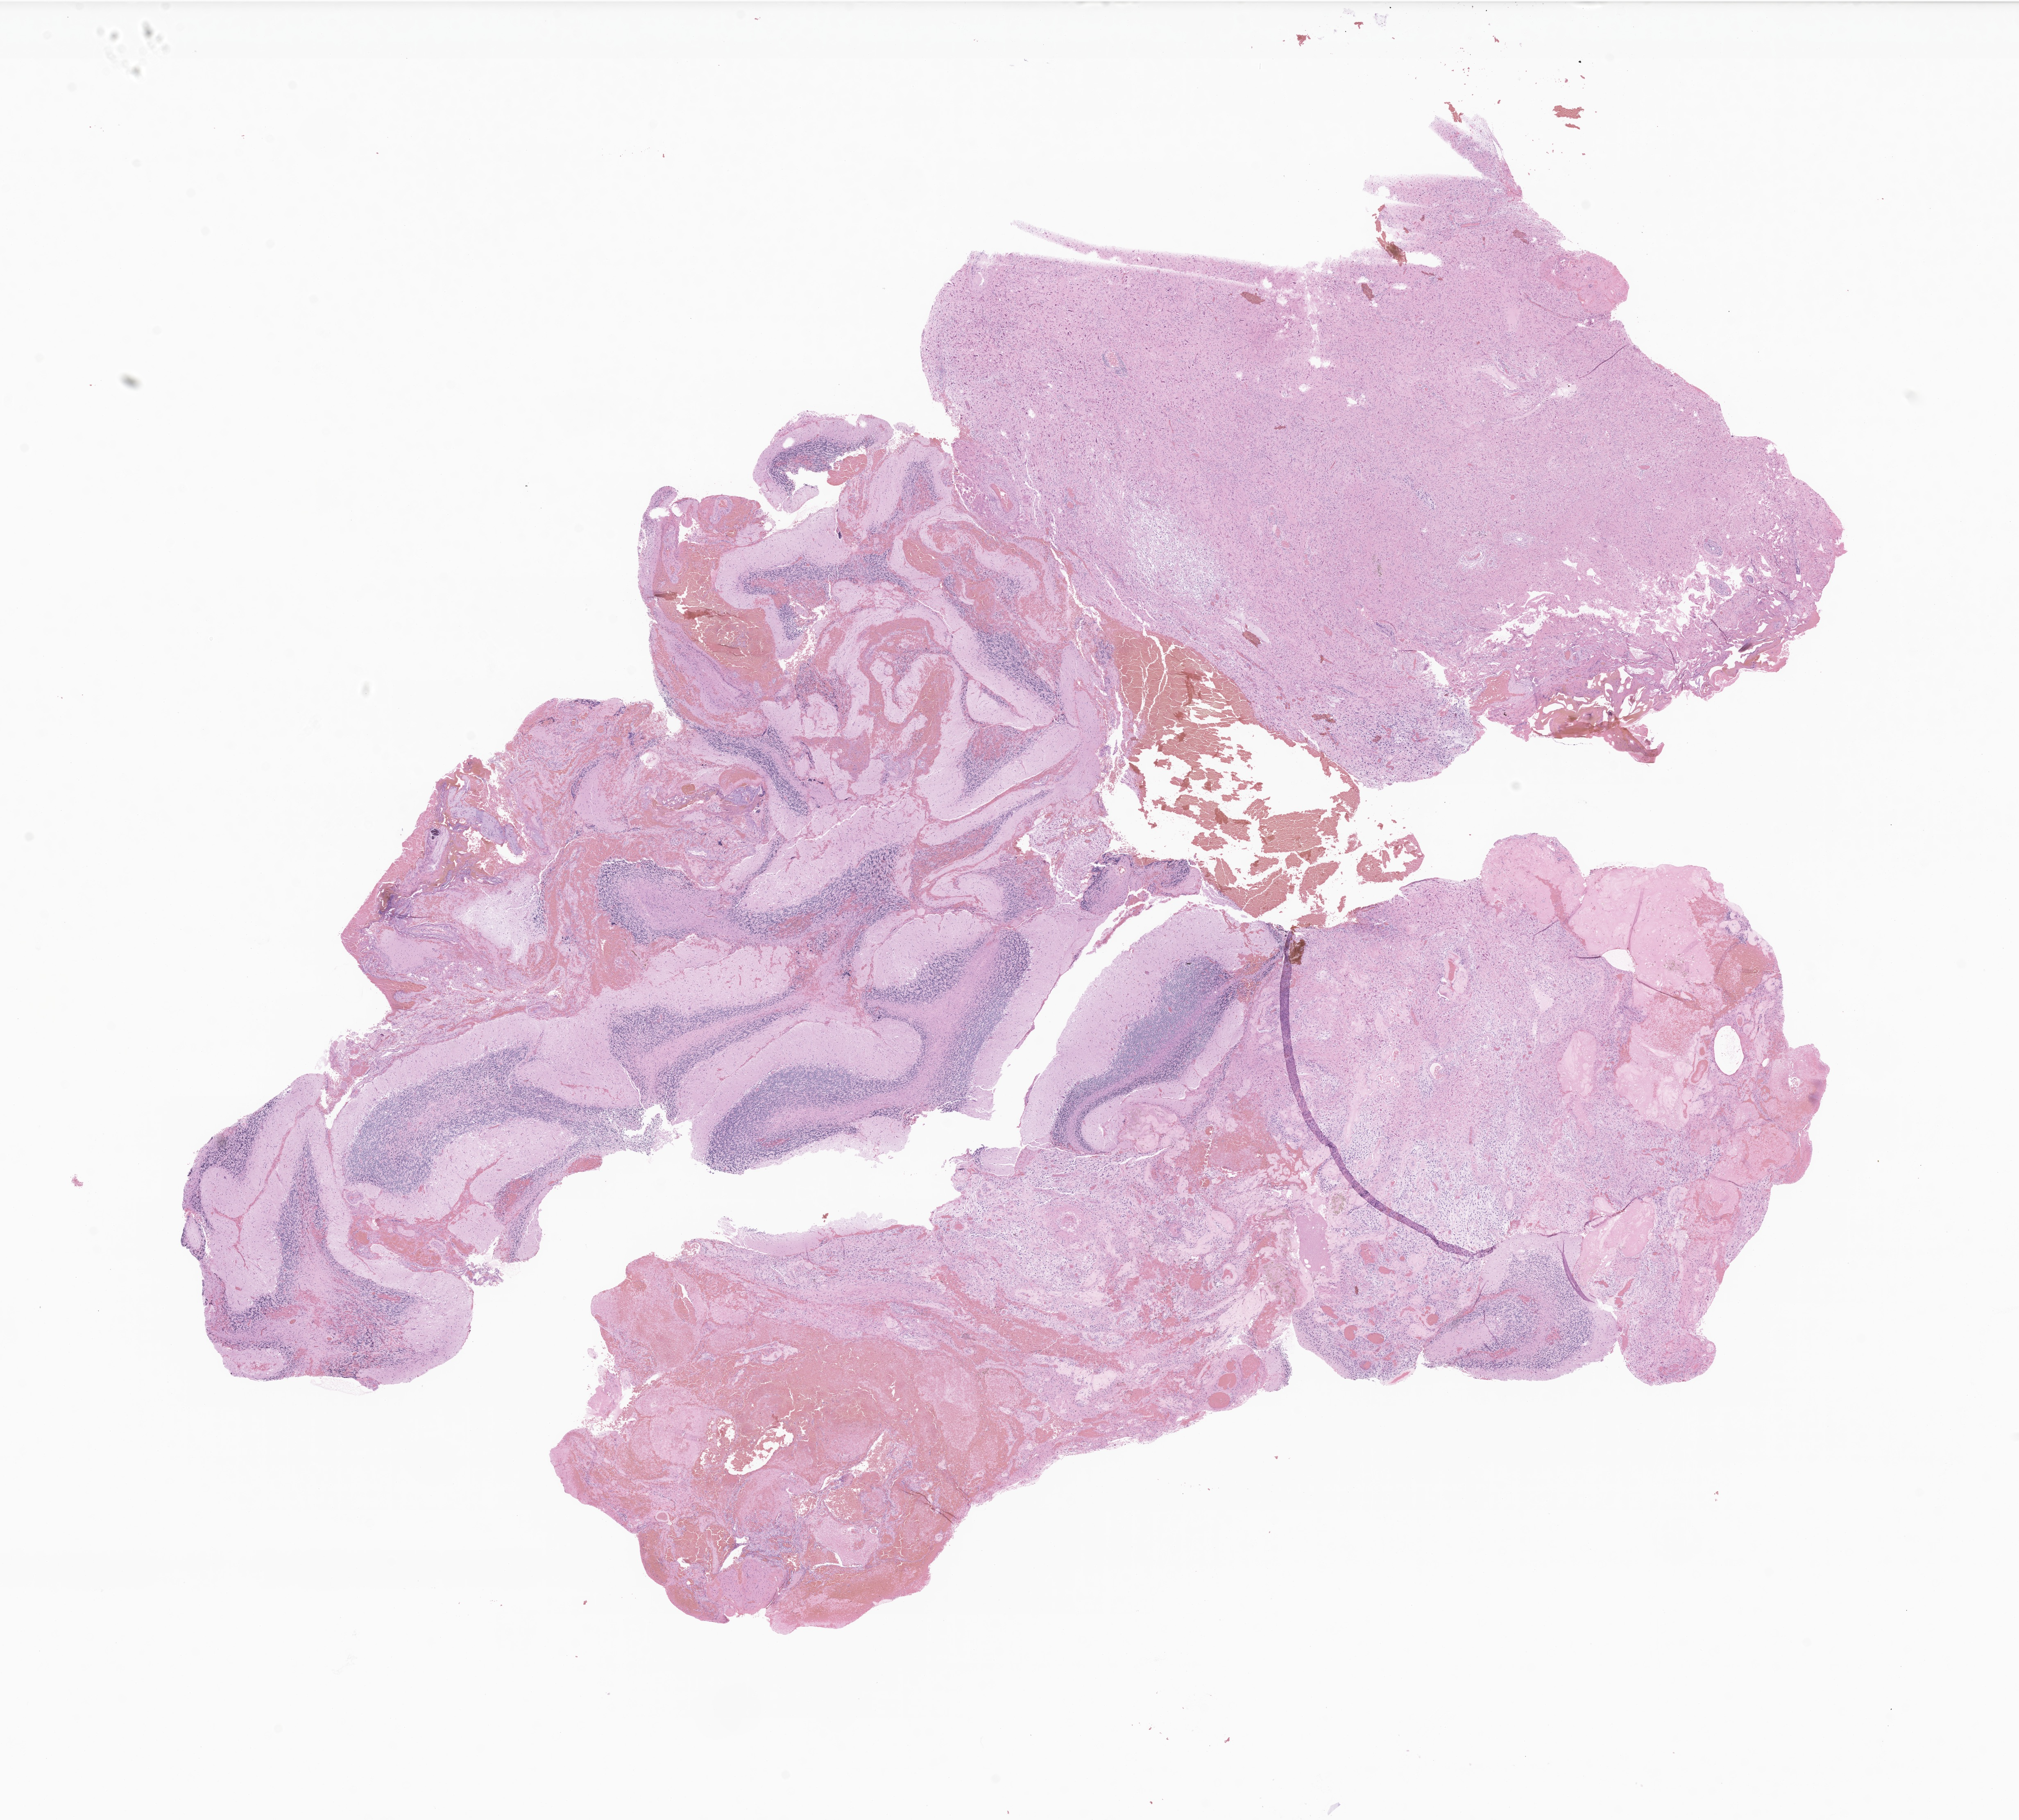
Digitized haematoxylin and eosin-stained section of tumor tissue from the brain, a low-resolution overview of the entire scanned area, about 20.8 x 18.7 mm, formalin-fixed, paraffin-embedded (FFPE) tissue. Male patient, age 177 months (14 years 9 months).
Diagnosis (ICD-O-3 morphology term): Neoplasm, uncertain whether benign or malignant.